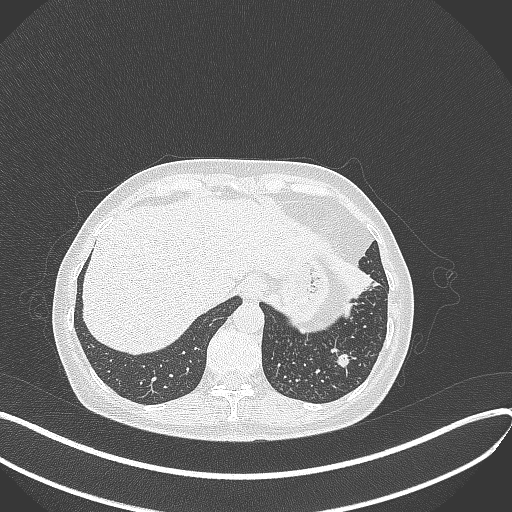
Chest CT, one axial slice. Reconstruction kernel B70f. 100 kVp. Lung window (W 1500 / L -600 HU). 1 mm slice thickness. 512 × 512 image matrix. Female patient, age 63 years. Case-level facts recorded for this patient, not image findings: clinical TNM (as recorded): T1b N0 M0.
Structures marked on this image (bounding box drawn by a radiologist):
- lung tumour (recorded histology: adenocarcinoma): bounding box (x1, y1, x2, y2) in pixels: (345, 262, 379, 300)